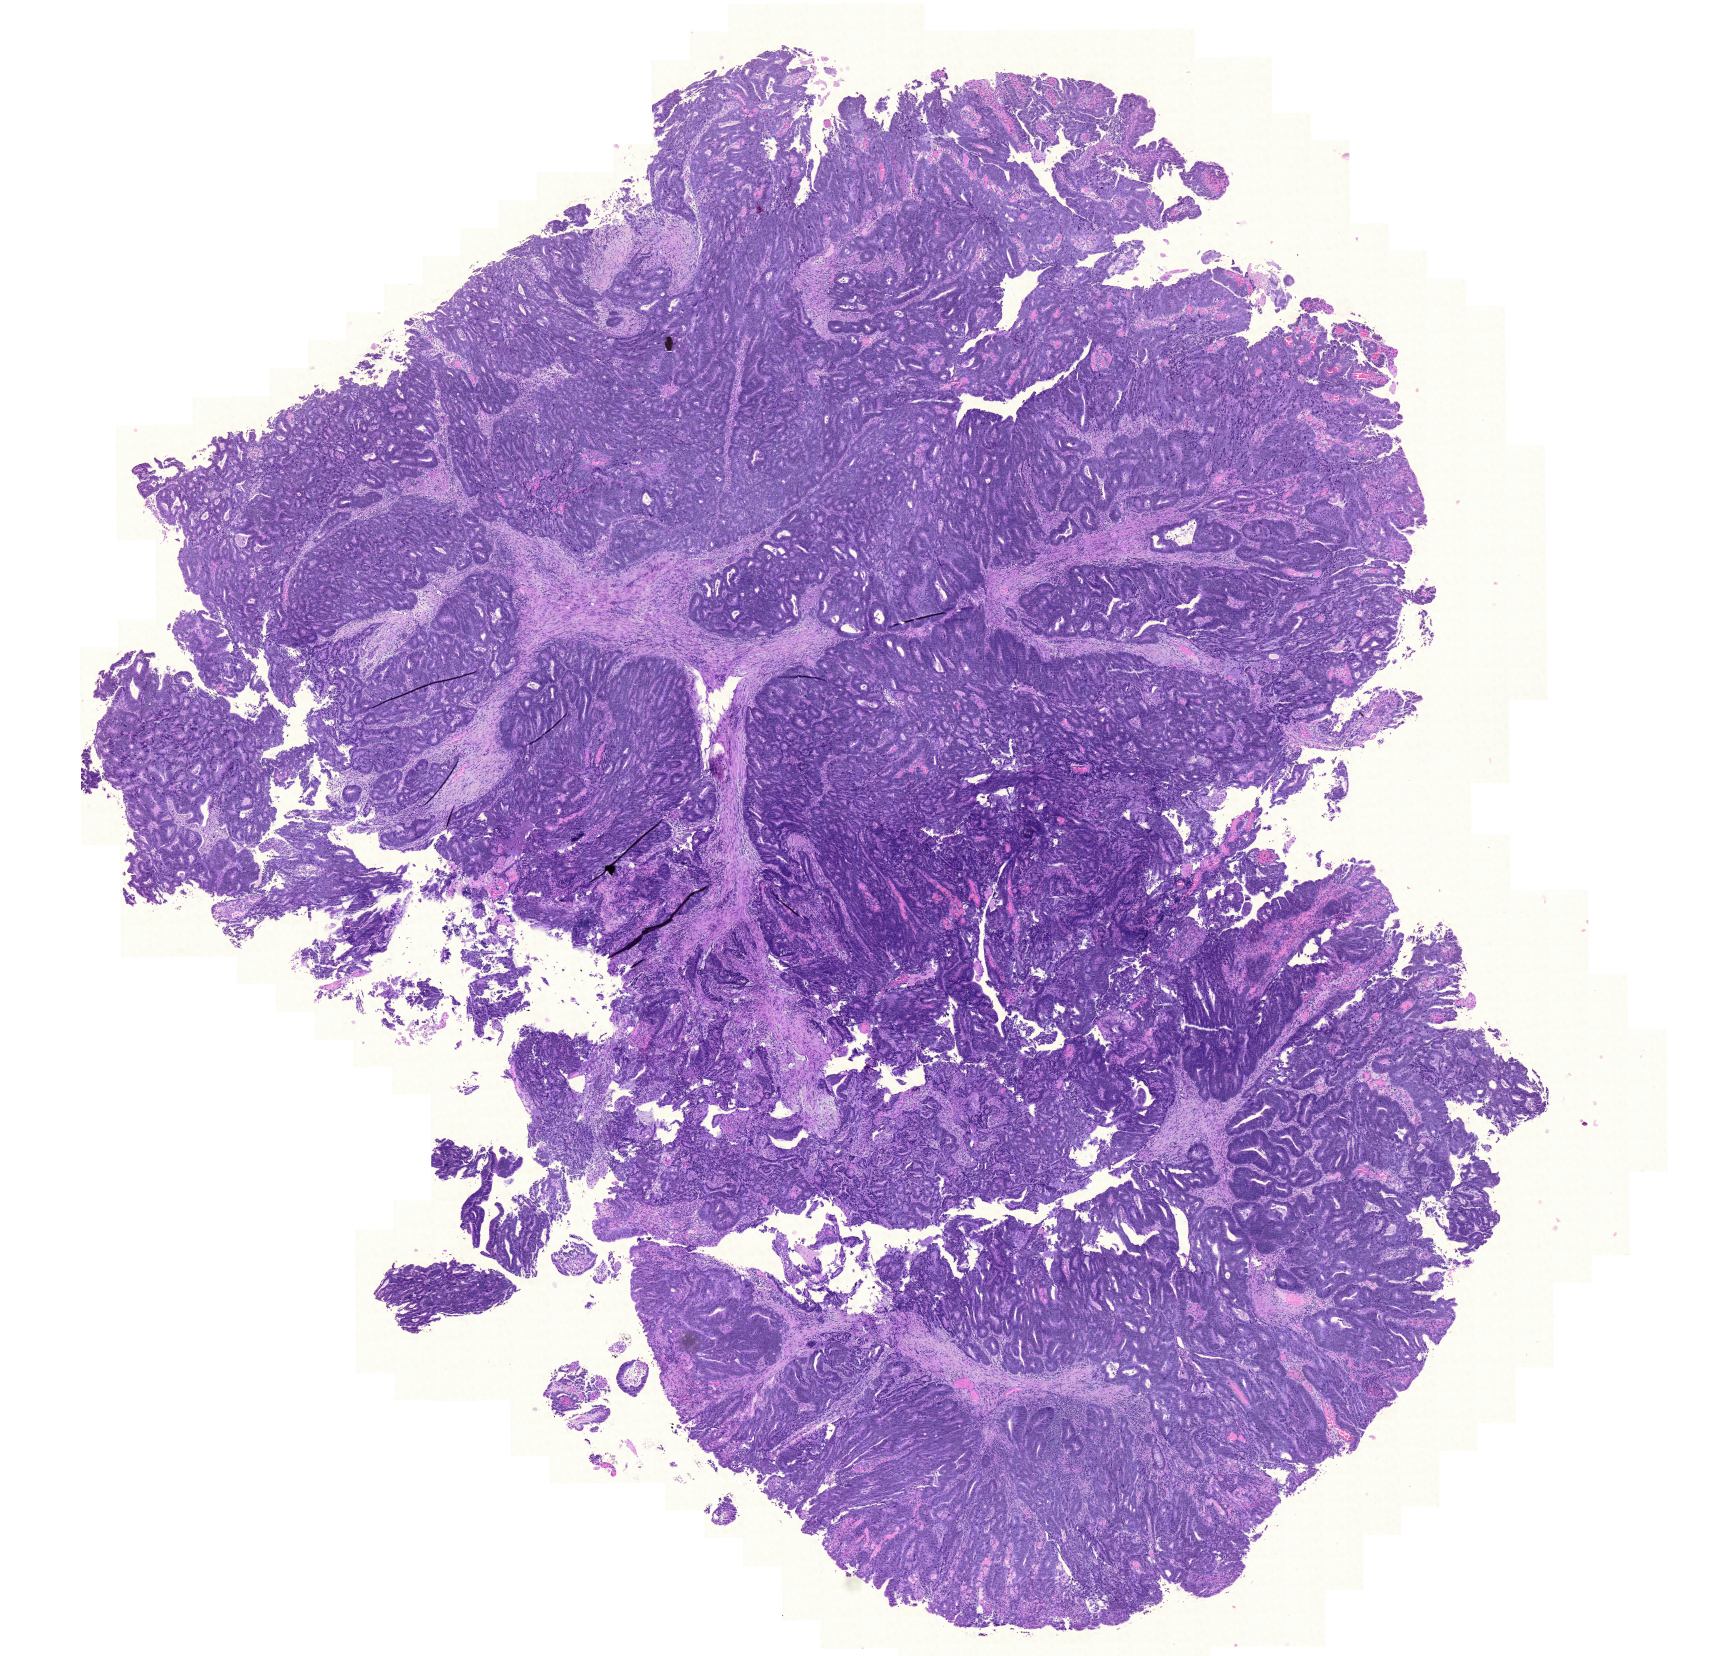
H&E whole-slide image, low-resolution overview of the scanned area, about 12.9 x 12.3 mm (from a 20x scan). Formalin-fixed paraffin-embedded (FFPE) diagnostic section. Rectum, primary tumour sample. Patient: male, age at initial diagnosis 66 years.
Lymph nodes positive (case pathology): 3 of 16 examined. TNM: T2 N1 M1. AJCC pathologic stage: IV (6th edition). Pathologic diagnosis: Adenocarcinoma, NOS.